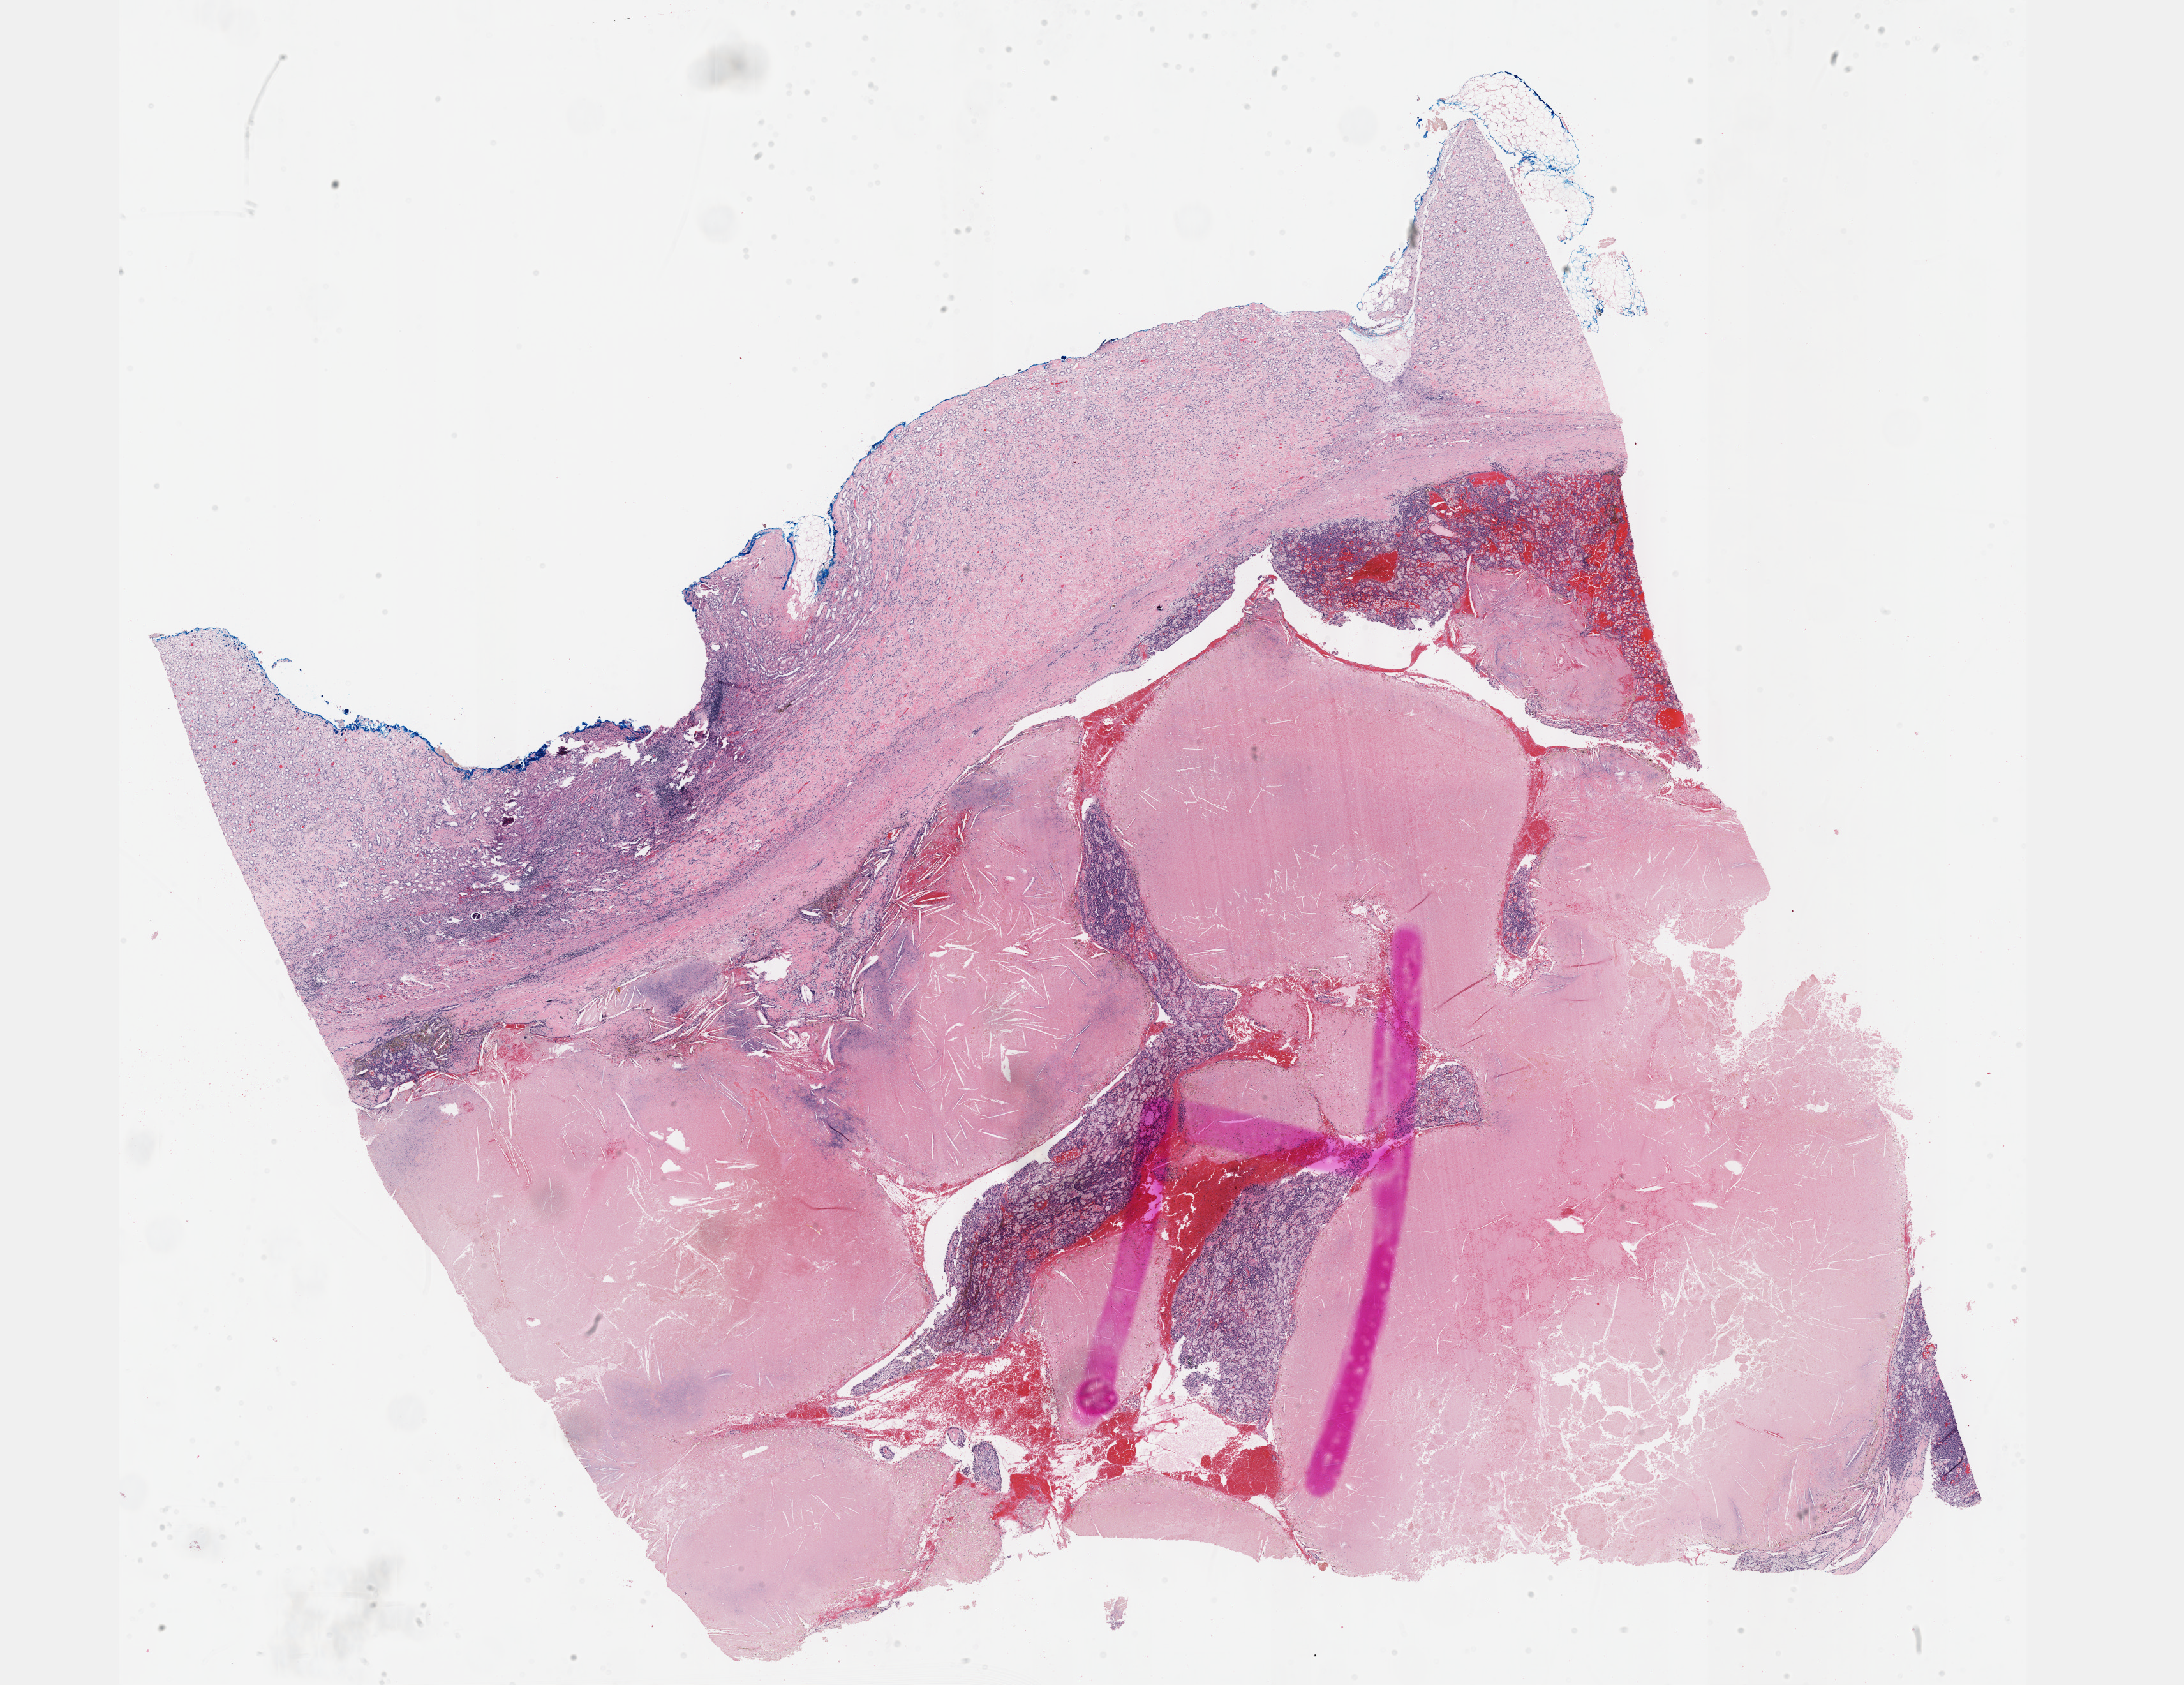
Hematoxylin and eosin (H&E) stained whole-slide image, whole scanned area (about 27.7 x 21.3 mm) shown as a low-resolution overview; FFPE section; sample: primary tumour, kidney. Patient: male, age at initial diagnosis 85 years.
Diagnosis: Papillary adenocarcinoma, NOS.